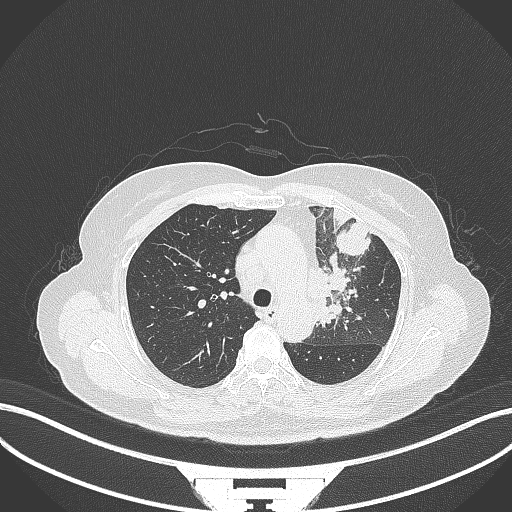
Chest CT, one axial slice; slice 237 of 382 in the series (ordered by position); 120 kVp; lung window (W 1500 / L -600 HU); 512 × 512 image matrix, field of view 400 × 400 mm. Female patient, age 64 years. From the clinical record (not read from this slice): clinical TNM (as recorded): T2a N2 M0.
Annotated regions visible in this slice (bounding box drawn by a radiologist):
- lung tumour (recorded histology: adenocarcinoma): bounding box (x1, y1, x2, y2) in pixels: (308, 252, 354, 330)
- lung tumour (recorded histology: adenocarcinoma): (335, 220, 373, 257)